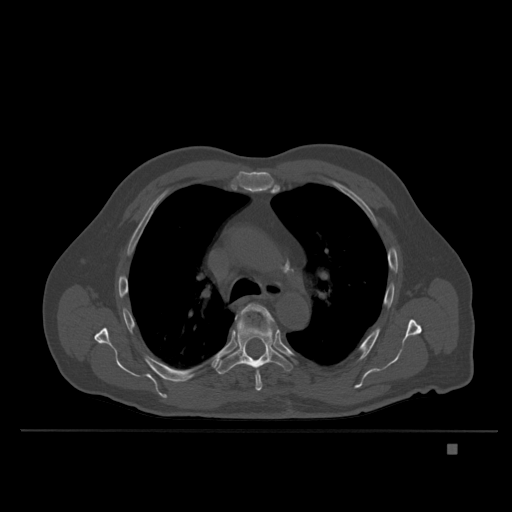
CT including the spine, one axial slice. Position 264 of 435 along the scan axis. Bone window (W 1800 / L 400 HU). 1.5 mm slice thickness. 512 × 512 image matrix. Patient: male, 73 years. From the clinical record (not read from this slice): primary cancer: skin.
Structures marked on this image (semi-automatically segmented with operator editing):
- T5 vertebra: bounding box <242,303,271,391> (left, top, right, bottom; pixels)
- T6 vertebra: <214,318,293,375>